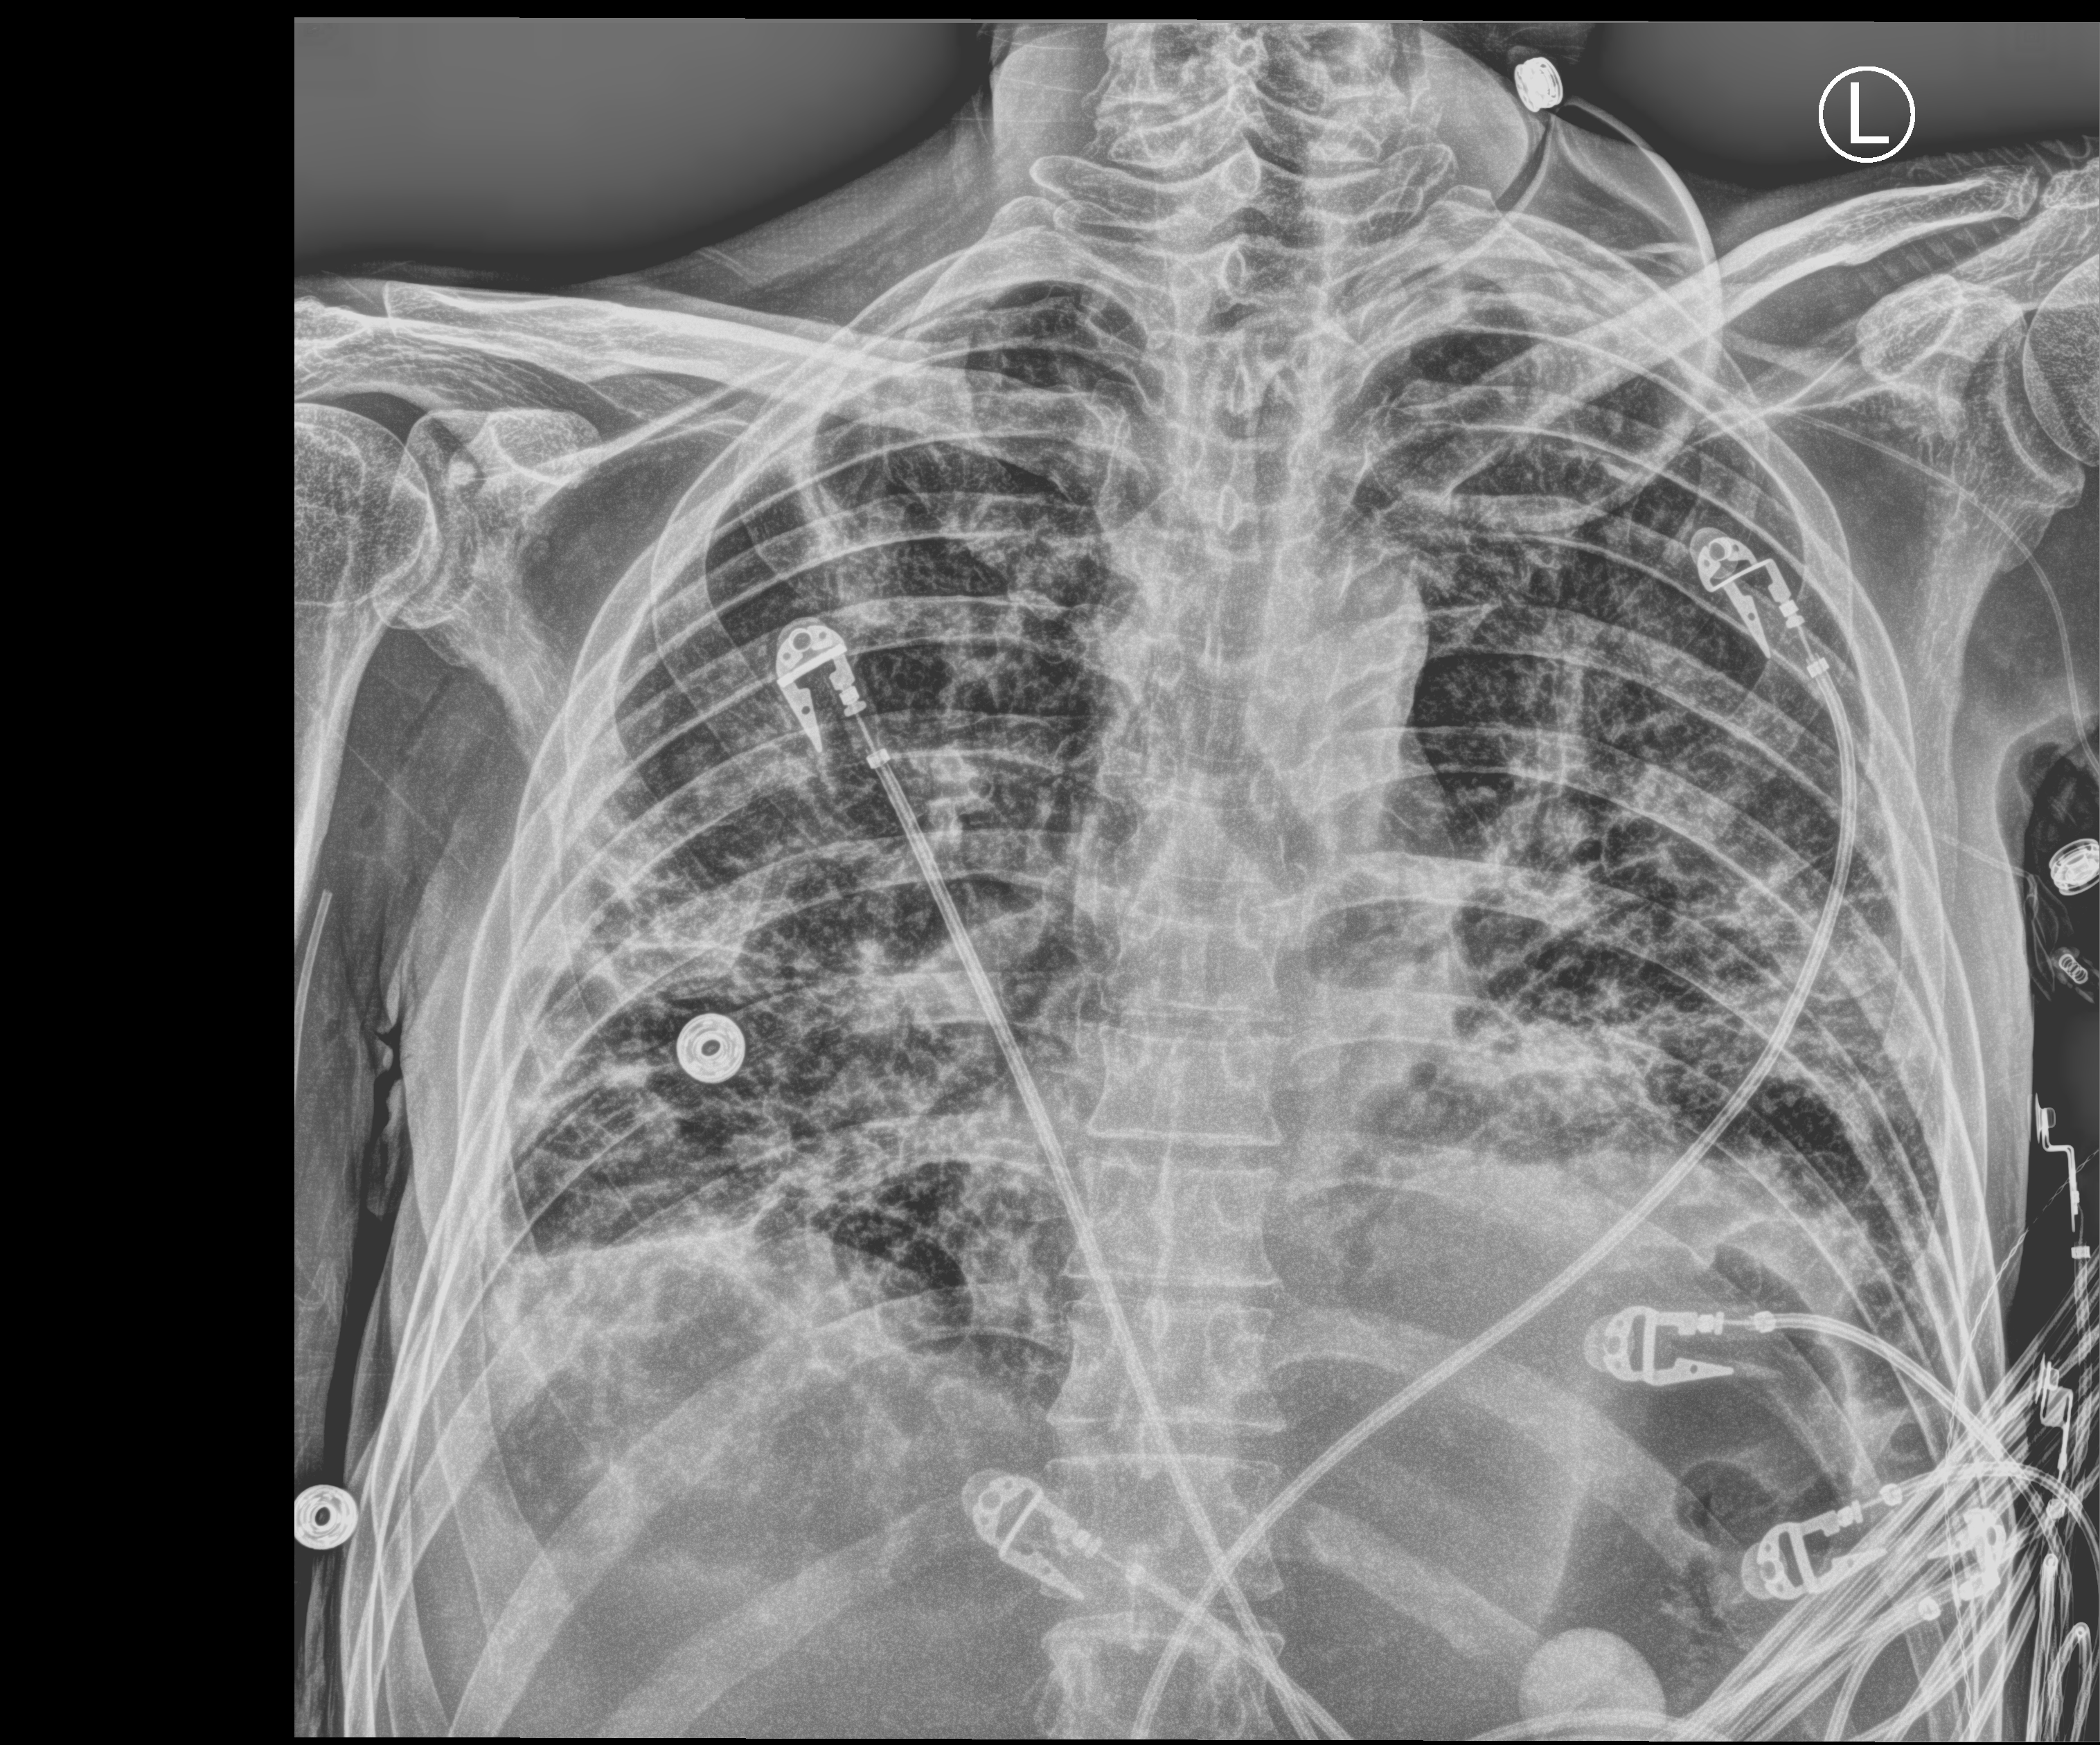
Portable chest radiograph, anteroposterior (AP) projection. Patient hospitalised with COVID-19; male, aged 18–59 years.
Hospital-stay facts (about this admission, not read from this image; timing relative to this image not recorded): chronic kidney disease (admission record): no; hypertension (admission record): yes.